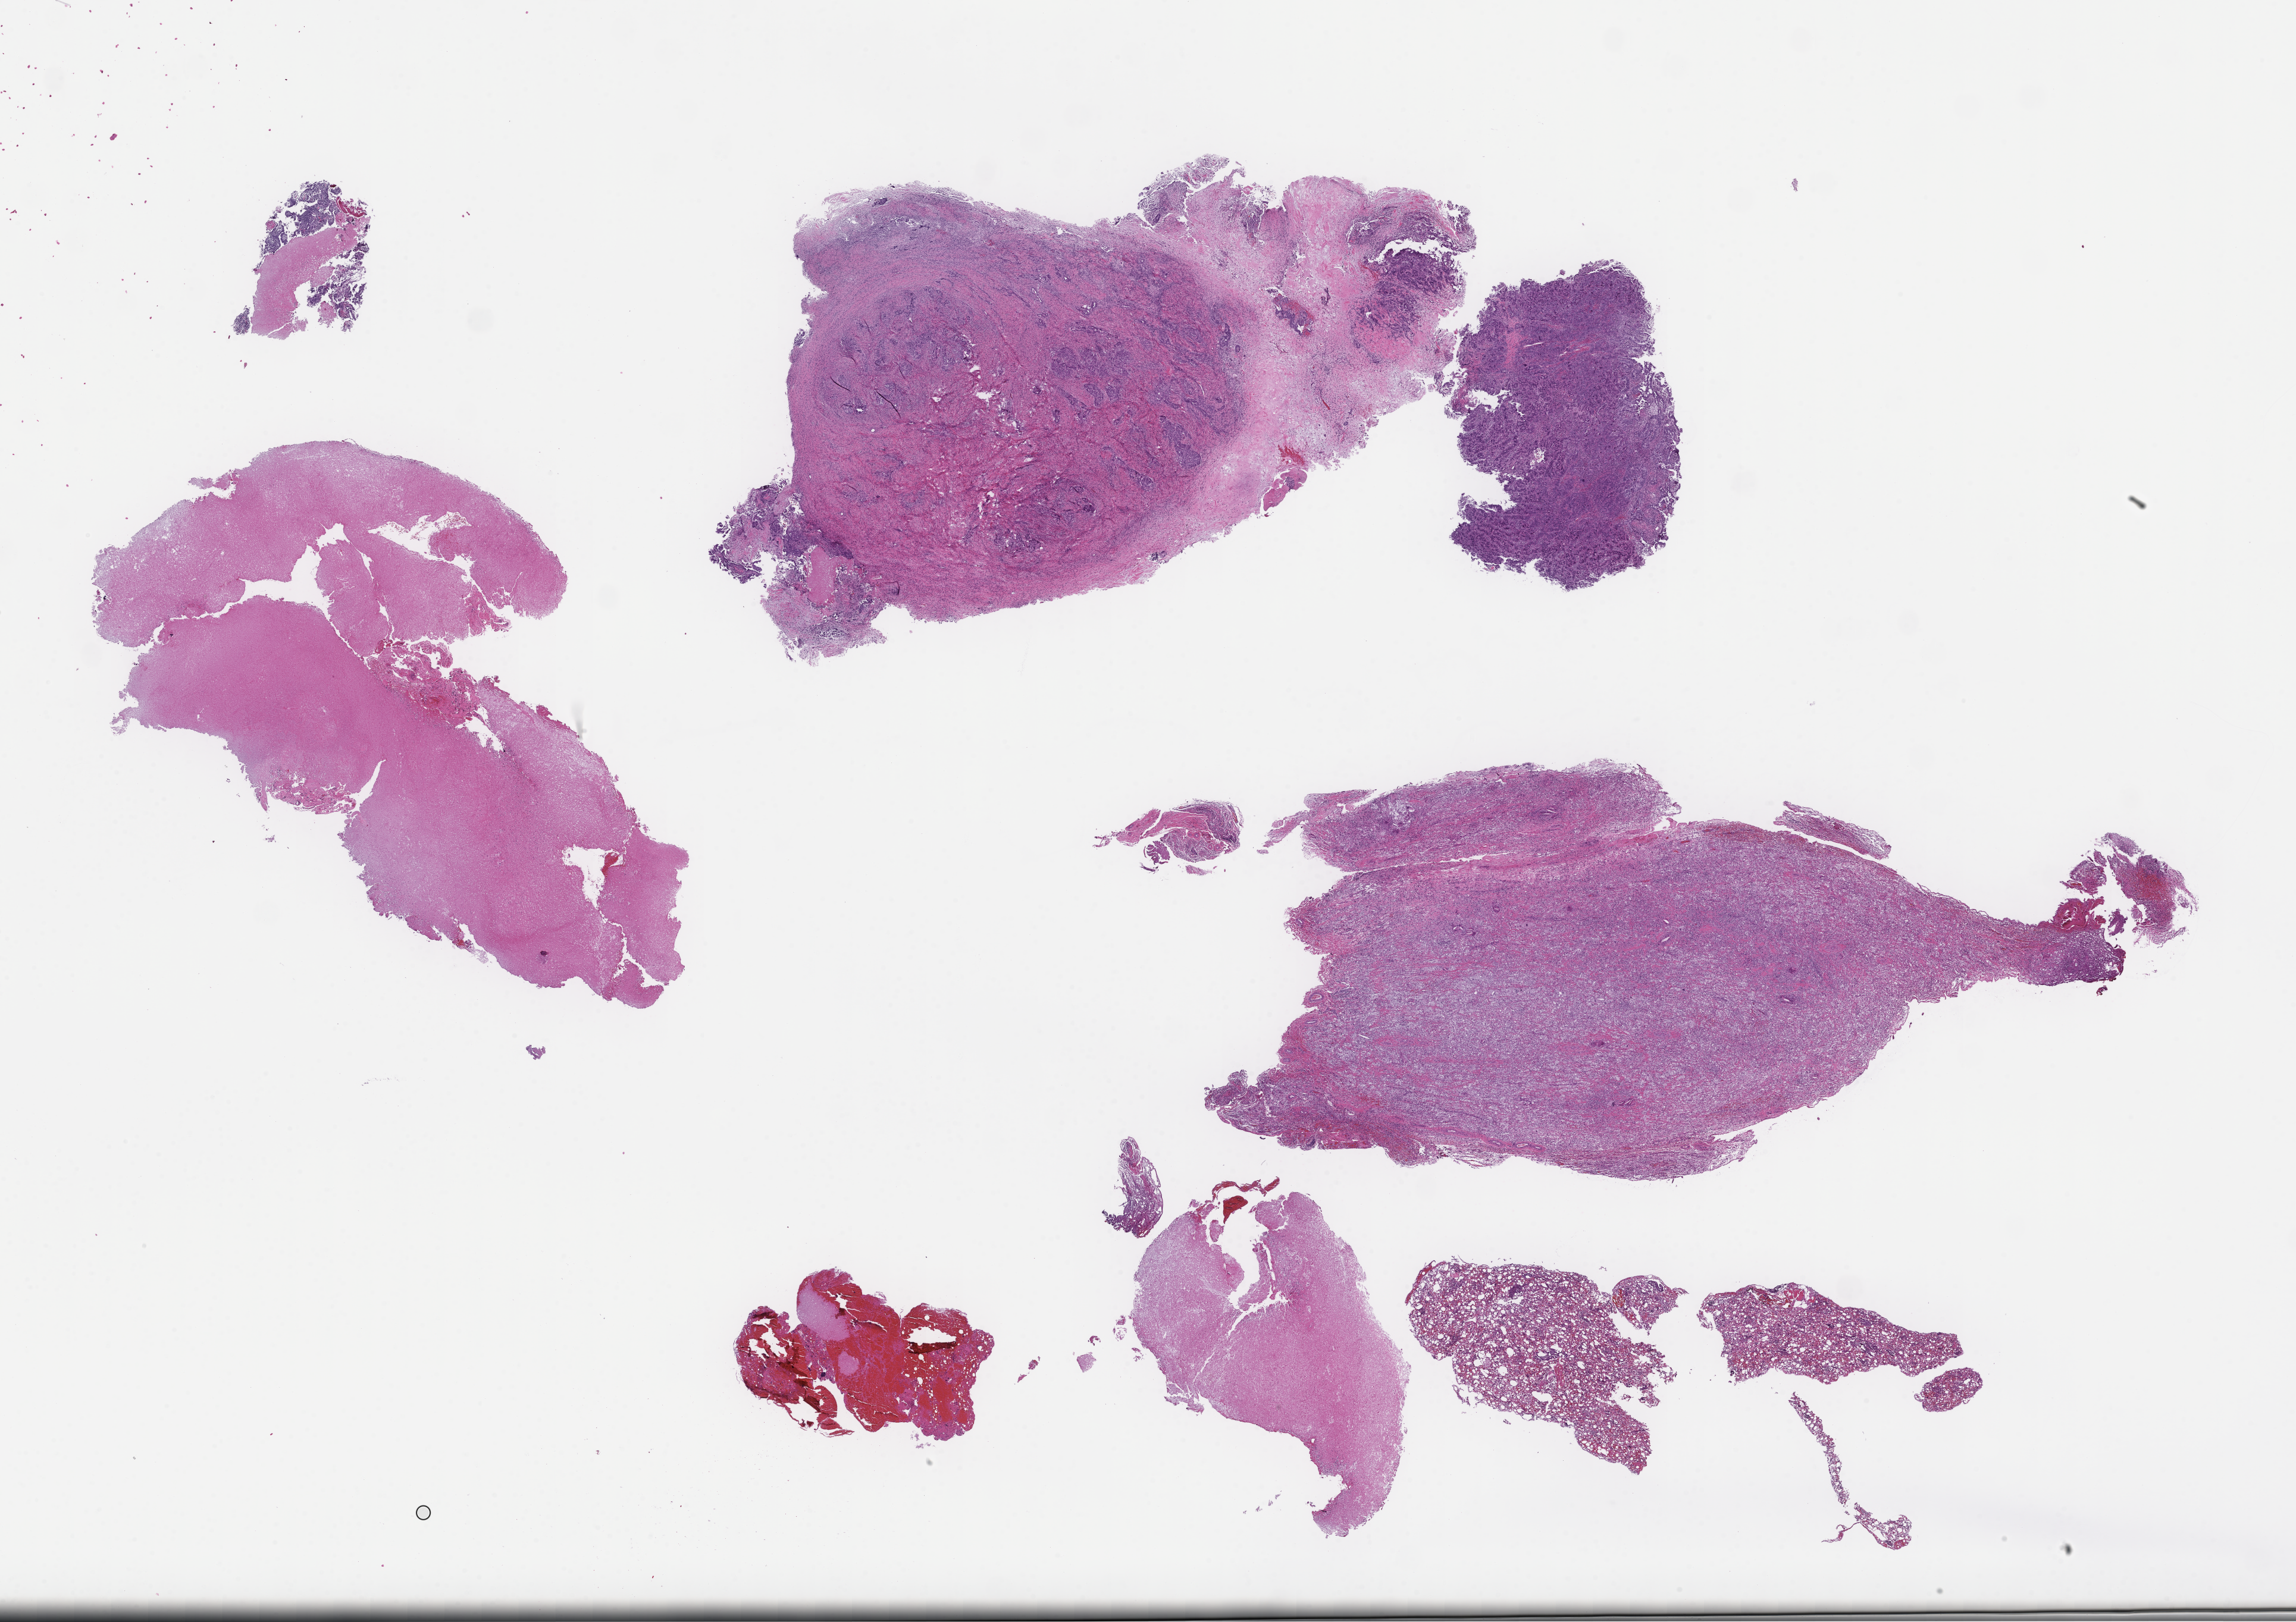
Haematoxylin and eosin whole-slide image, low-resolution overview of the scanned area, about 31.2 x 22.0 mm; FFPE section; tissue site: ovary; collected on treatment. Patient: female.
This section: primary tumor. Diagnosis: Ovarian Carcinoma.